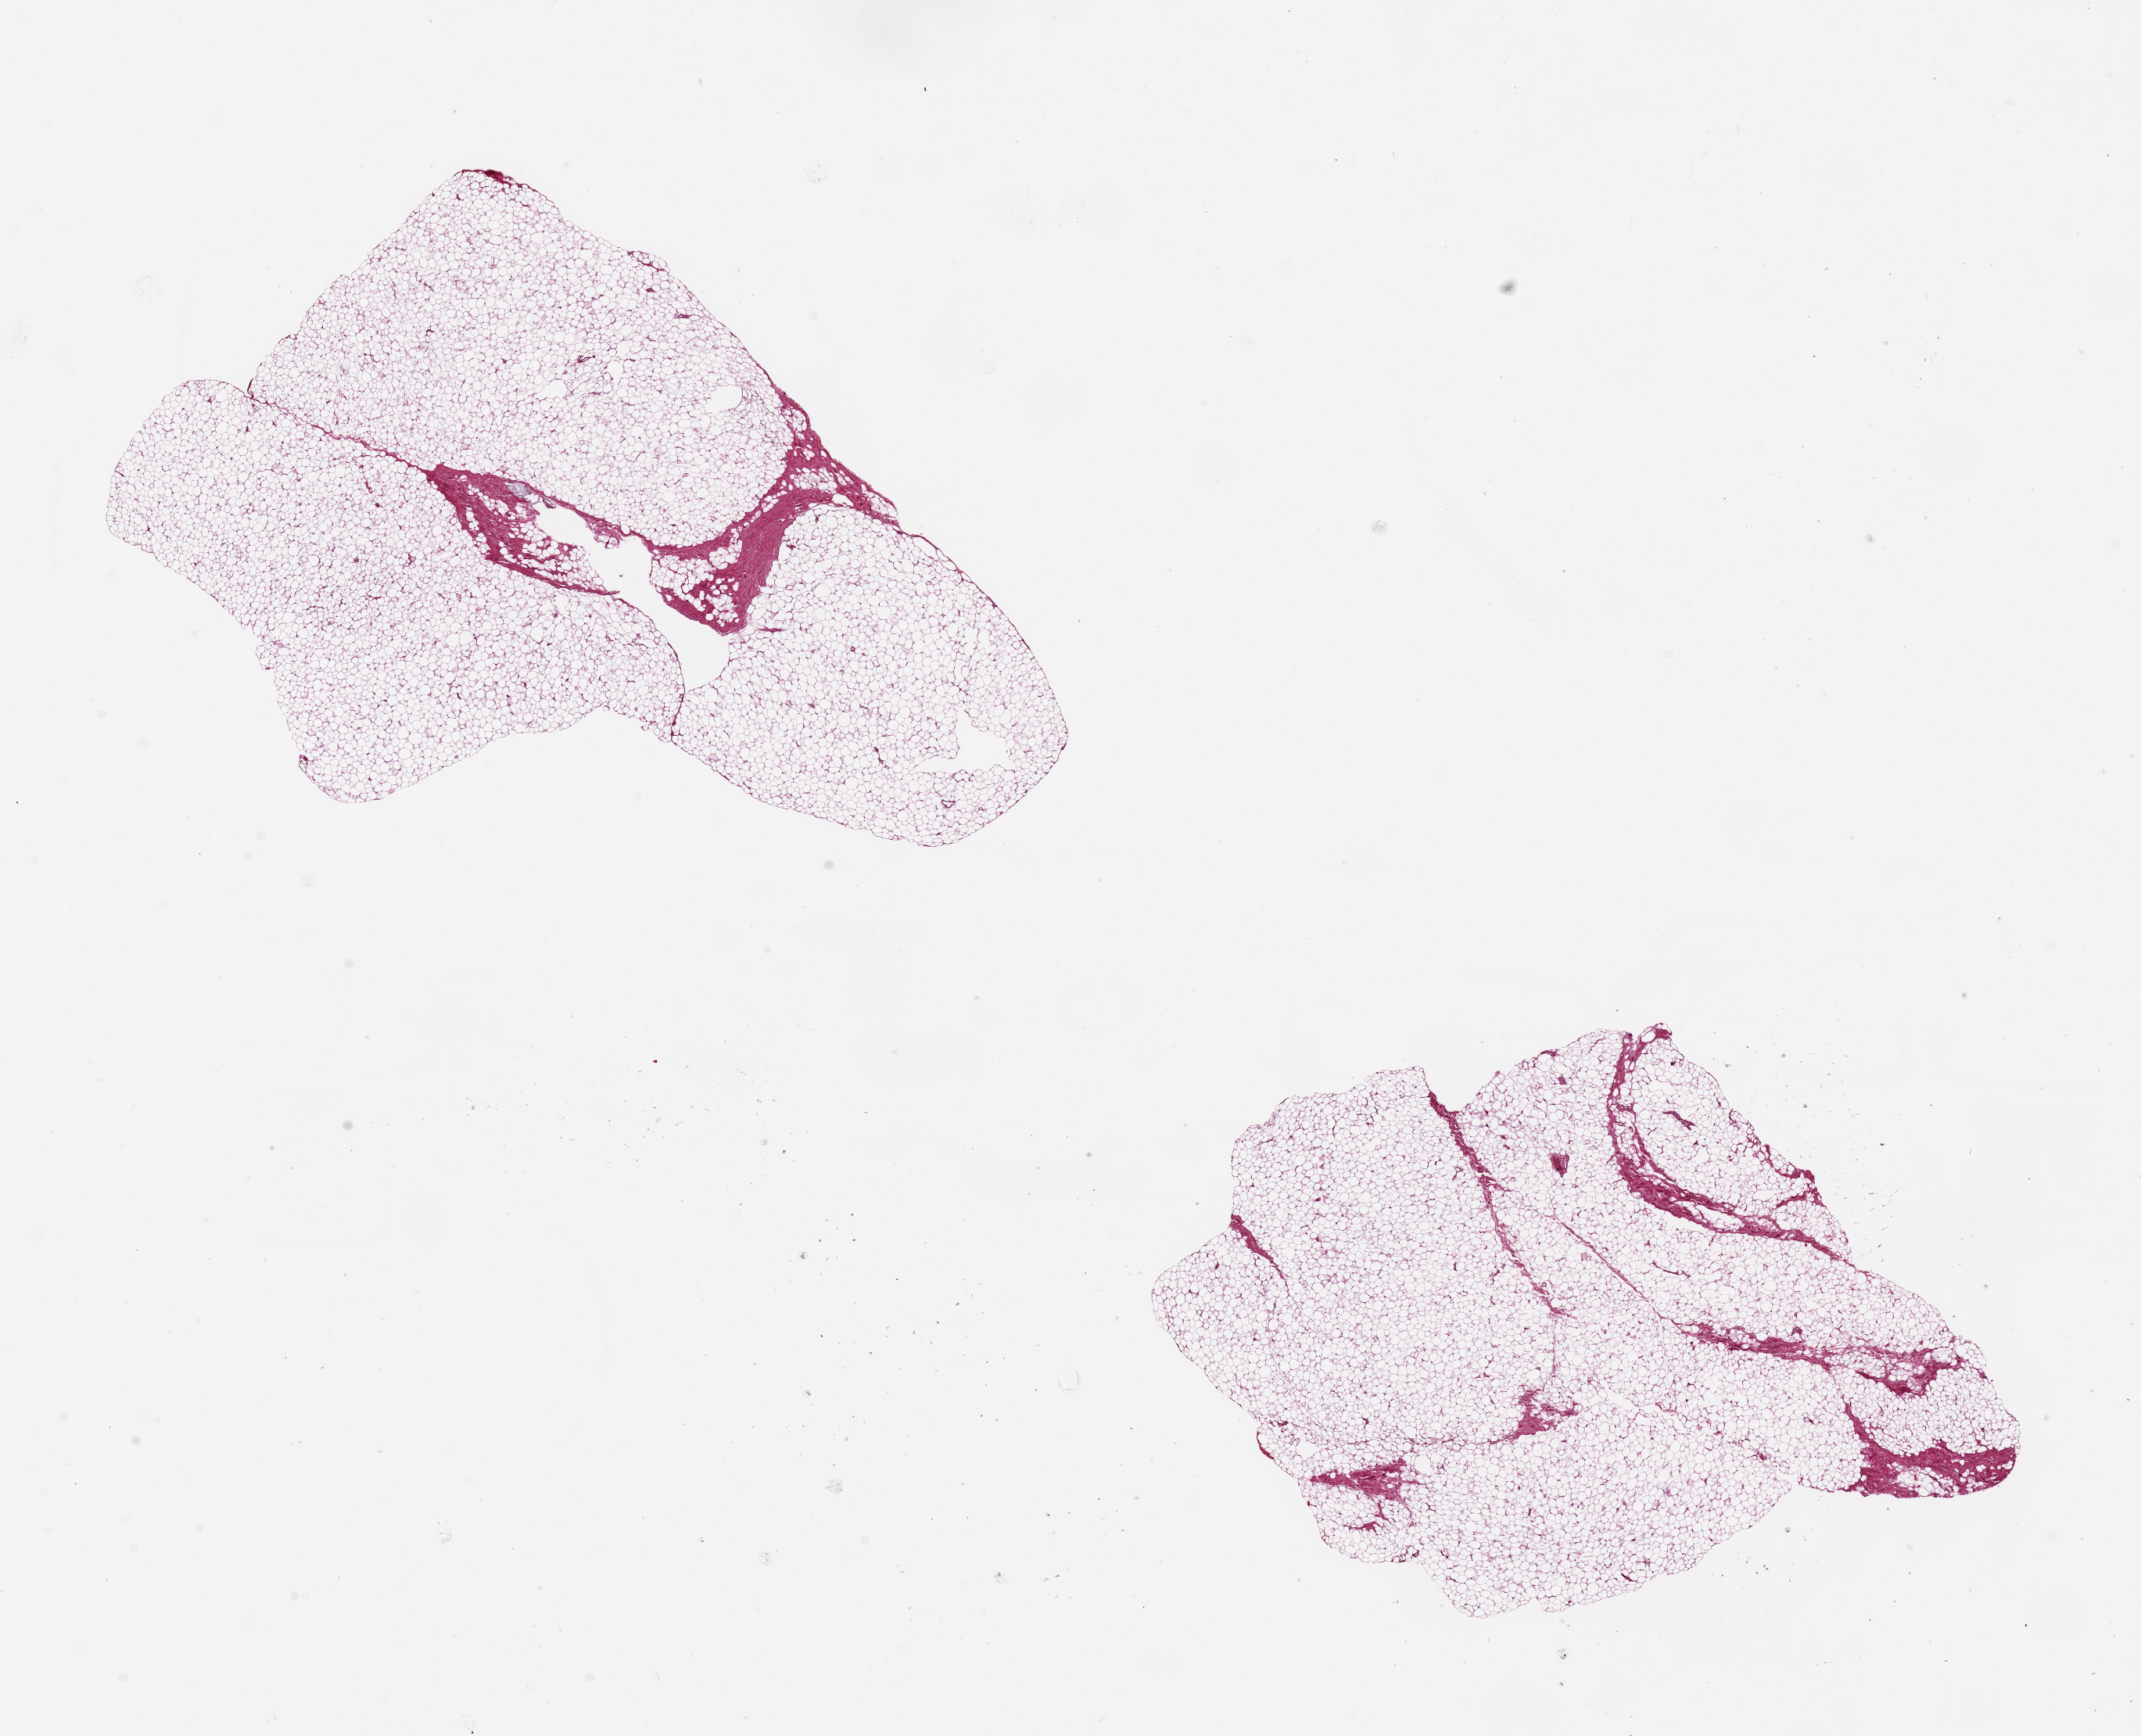
Whole-slide image, H&E stain, brightfield, a low-resolution overview of the entire scanned area, about 21.7 x 17.6 mm; PAXgene-fixed, paraffin-embedded tissue; section of breast (target tissue); tissue donor sample.
- reviewer comment on this tissue sample: 2 ~7x5mm pieces, all fat/parenchyma; no ductal elements